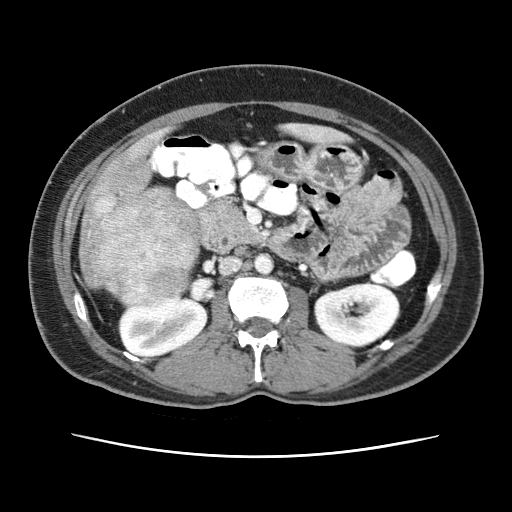
Contrast-enhanced abdominal CT (liver protocol), one axial slice; slice 12 of 79 in the series (ordered by position); reconstruction kernel STANDARD; 120 kVp; soft-tissue window (W 400 / L 40 HU); 2.5 mm slice thickness; 512 × 512 image matrix, field of view 340 × 340 mm. From the clinical record (not read from this slice): diagnosis: hepatocellular carcinoma (patient treated with transarterial chemoembolisation; whether this scan precedes or follows treatment is not stated here); TNM stage (as recorded): Stage-I; Child-Pugh class: A; tumour differentiation: moderately differentiated; tumour nodularity: uninodular.
Structures marked on this image (semi-automatically segmented with operator editing):
- abdominal aorta: bounding box <255,254,273,274> (left, top, right, bottom; pixels)
- liver parenchyma outside the tumour (the mass and vessels are separate outlines, so this box may not span the whole liver): <80,134,211,286>
- mass: <79,179,202,305>